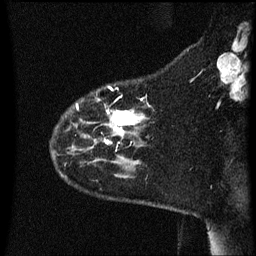
Breast MRI (dynamic contrast-enhanced), one sagittal slice; position 12 of 60 along the scan axis; dynamic contrast-enhanced series, image 2 of 3 at this slice position (ordered by acquisition); 1.5 T; TE 4.2 ms, TR 8.4 ms; 2.2 mm slice thickness; 256 × 256 image matrix, field of view 200 × 200 mm. Patient: female, 35 years. Case-level facts recorded for this patient, not image findings: setting: breast cancer imaged before/during neoadjuvant chemotherapy; receptor status: HER2-positive.
Outlined on this slice (semi-automatically segmented with operator editing):
- analysis volume of interest (the breast-tissue region the enhancement analysis was run in; not a lesion): bounding box [x1, y1, x2, y2] px = [53, 86, 151, 163]
- tumour enhancement mask (voxels above the 70 % enhancement threshold inside the analysis volume of interest): [105, 110, 140, 141]